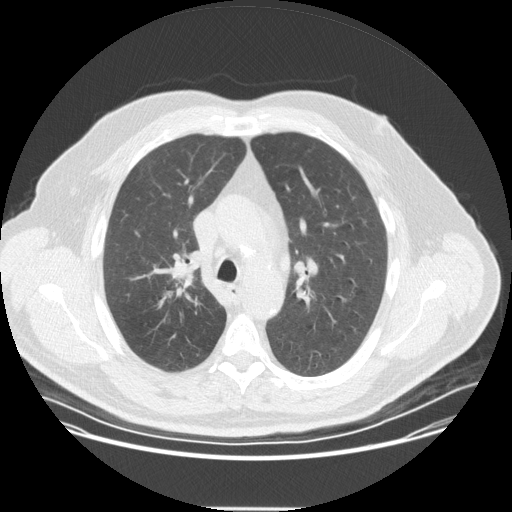
Low-dose screening chest CT, one axial slice. Slice 237 of 351 in the series (ordered by position). 120 kVp. Lung window (W 1500 / L -600 HU). 2.5 mm slice thickness. 512 × 512 image matrix, field of view 419 × 419 mm.
Structures marked on this image (manually delineated by an expert):
- lesion 1 (tumor, upper lobe of right lung): bounding box (x1, y1, x2, y2) in pixels: (170, 266, 196, 288)